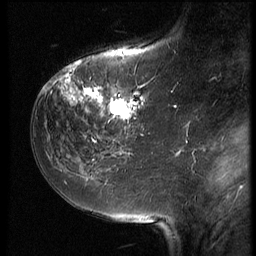
Breast MRI (dynamic contrast-enhanced), one sagittal slice. Position 20 of 64 along the scan axis. 3 images stored at this slice position (order not interpretable as contrast timing). 1.5 T. TE 4.2 ms, TR 9 ms. 2.5 mm slice thickness. 256 × 256 image matrix, field of view 180 × 180 mm. Female patient, age 59 years. From the clinical record (not read from this slice): setting: breast cancer imaged before/during neoadjuvant chemotherapy; receptor status: HER2-positive.
Structures marked on this image (semi-automatically segmented with operator editing):
- analysis volume of interest (the breast-tissue region the enhancement analysis was run in; not a lesion): box from (x=54, y=65) to (x=155, y=132) px
- tumour enhancement mask (voxels above the 140 % enhancement threshold inside the analysis volume of interest): (x=54, y=65)–(x=147, y=121)